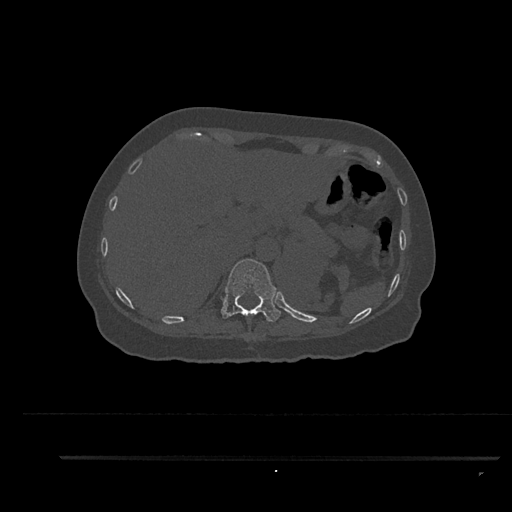
CT including the spine, one axial slice. Slice 321 of 797 in the series (ordered by position). 120 kVp. Bone window (W 1800 / L 400 HU). 0.5 mm slice thickness. 512 × 512 image matrix, field of view 408 × 408 mm. Patient: female, 44 years. From the clinical record (not read from this slice): primary cancer: renal; vertebrae with lytic lesions (as recorded): L1.
Structures marked on this image (semi-automatically segmented with operator editing):
- T11 vertebra: bounding box [x1, y1, x2, y2] px = [221, 259, 281, 322]